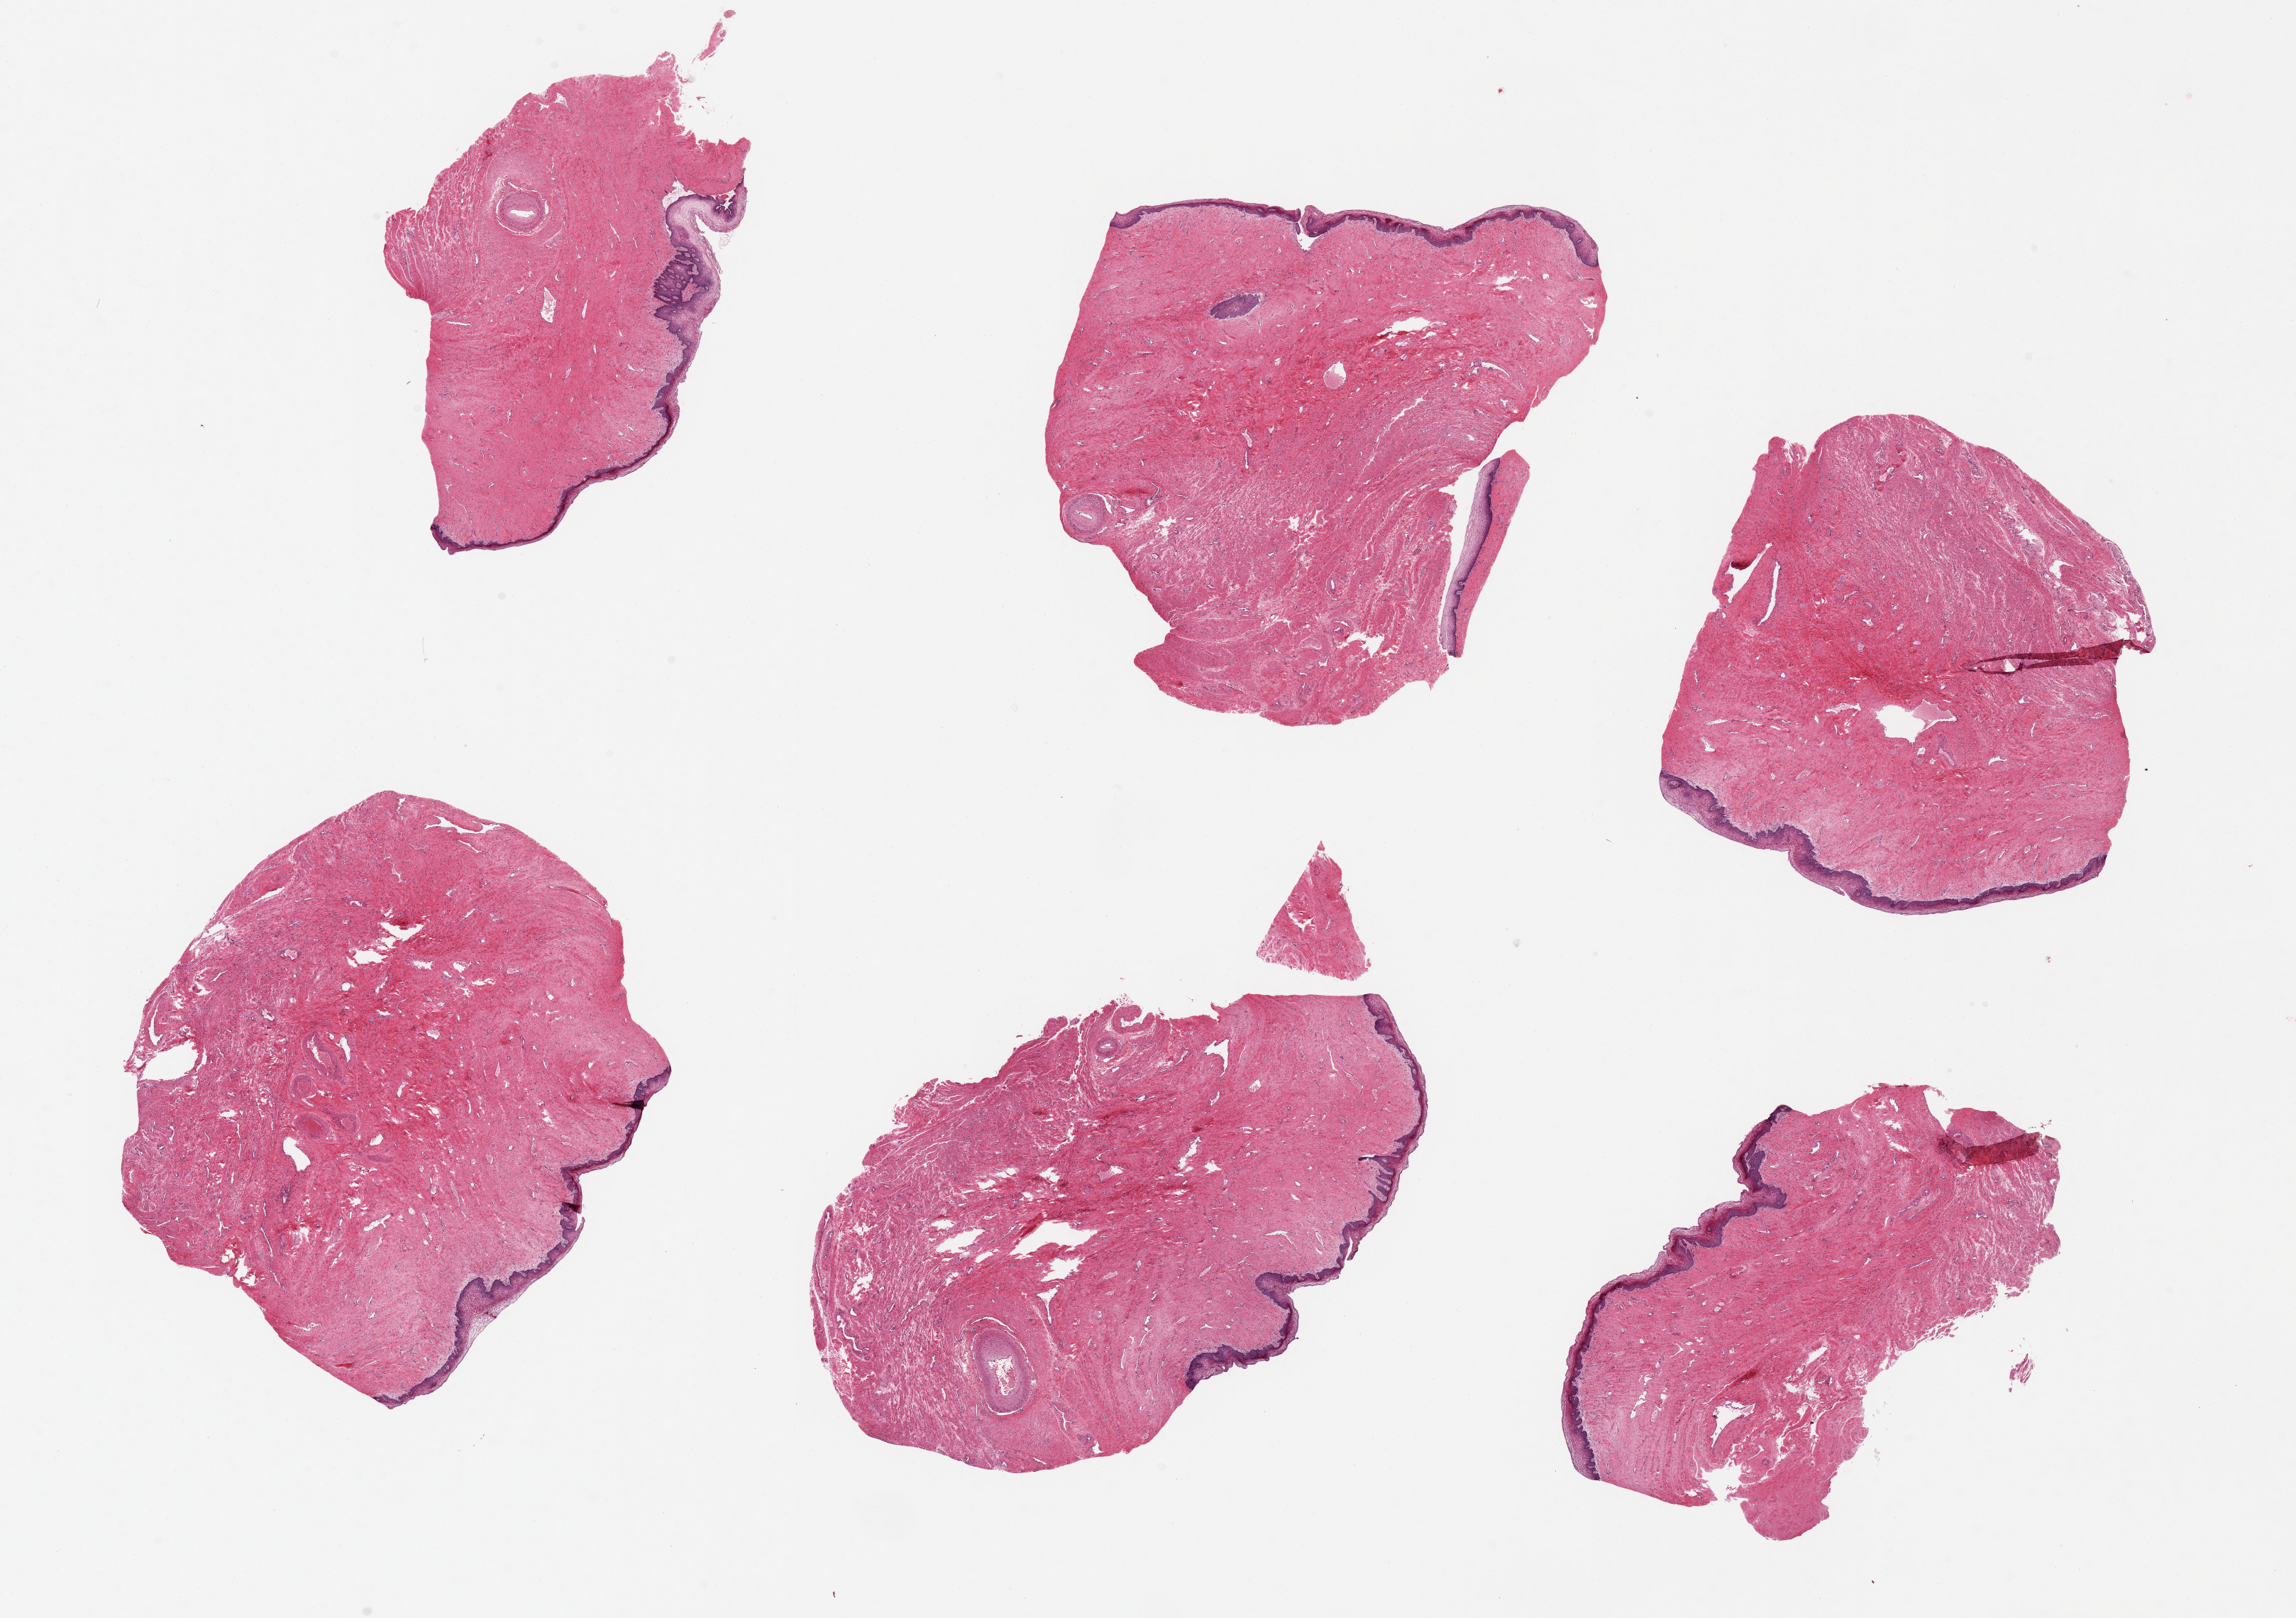
Whole-slide image, H&E stain, brightfield — whole scanned area (about 25.6 x 18.0 mm) shown as a low-resolution overview. PAXgene-fixed, paraffin-embedded tissue. Section of vagina (target tissue). Tissue donor sample. Donor: female.
• reviewer comment on this tissue sample: 6 pieces up to 7x4 mm; good mucosal preservation